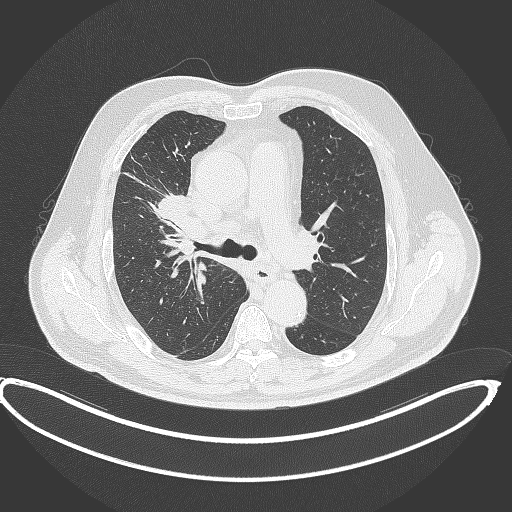
Chest CT, one axial slice. Slice 265 of 390 in the series (ordered by position). Reconstruction kernel B70f. 120 kVp. Lung window (W 1500 / L -600 HU). 1 mm slice thickness. 512 × 512 image matrix. Male patient, age 62 years. From the clinical record (not read from this slice): clinical TNM (as recorded): T1c N3 M1c.
Outlined on this slice (rectangle marked by the reading radiologist):
- lung tumour (recorded histology: adenocarcinoma): bounding box <154,192,200,230> (left, top, right, bottom; pixels)